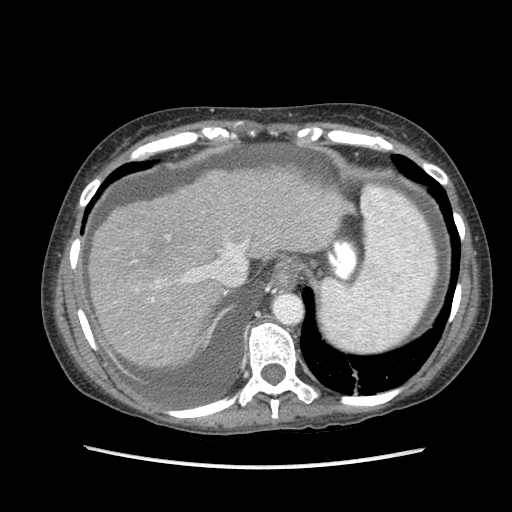
Contrast-enhanced abdominal CT (liver protocol), one axial slice. Slice 73 of 87 in the series (ordered by position). Reconstruction kernel STANDARD. 120 kVp. Soft-tissue window (W 400 / L 40 HU). 512 × 512 image matrix, field of view 340 × 340 mm. From the clinical record (not read from this slice): diagnosis: hepatocellular carcinoma (patient treated with transarterial chemoembolisation; whether this scan precedes or follows treatment is not stated here); TNM stage (as recorded): Stage-IIIB; Child-Pugh class: A; tumour differentiation: no biopsy; tumour nodularity: uninodular.
Outlined on this slice (semi-automatically segmented with operator editing):
- liver parenchyma outside the tumour (the mass and vessels are separate outlines, so this box may not span the whole liver): bounding box <90,168,351,366> (left, top, right, bottom; pixels)
- liver vessels: <136,236,247,302>